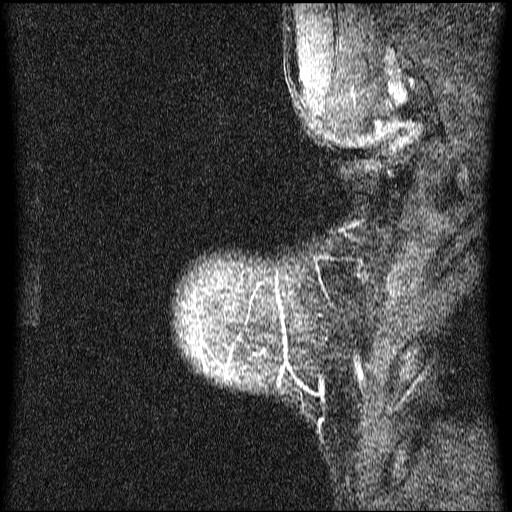
Breast MRI (dynamic contrast-enhanced), one sagittal slice; dynamic contrast-enhanced series, image 2 of 4 at this slice position (ordered by acquisition); 1.5 T; TE 4.2 ms, TR 9.1 ms; 2 mm slice thickness; 512 × 512 image matrix, field of view 180 × 180 mm. Female patient, age 33 years.
Annotated regions visible in this slice (semi-automatically segmented with operator editing):
- analysis volume of interest (the breast-tissue region the enhancement analysis was run in; not a lesion): box from (x=180, y=262) to (x=312, y=404) px
- tumour enhancement mask (voxels above the 70 % enhancement threshold inside the analysis volume of interest): (x=200, y=348)–(x=234, y=375)